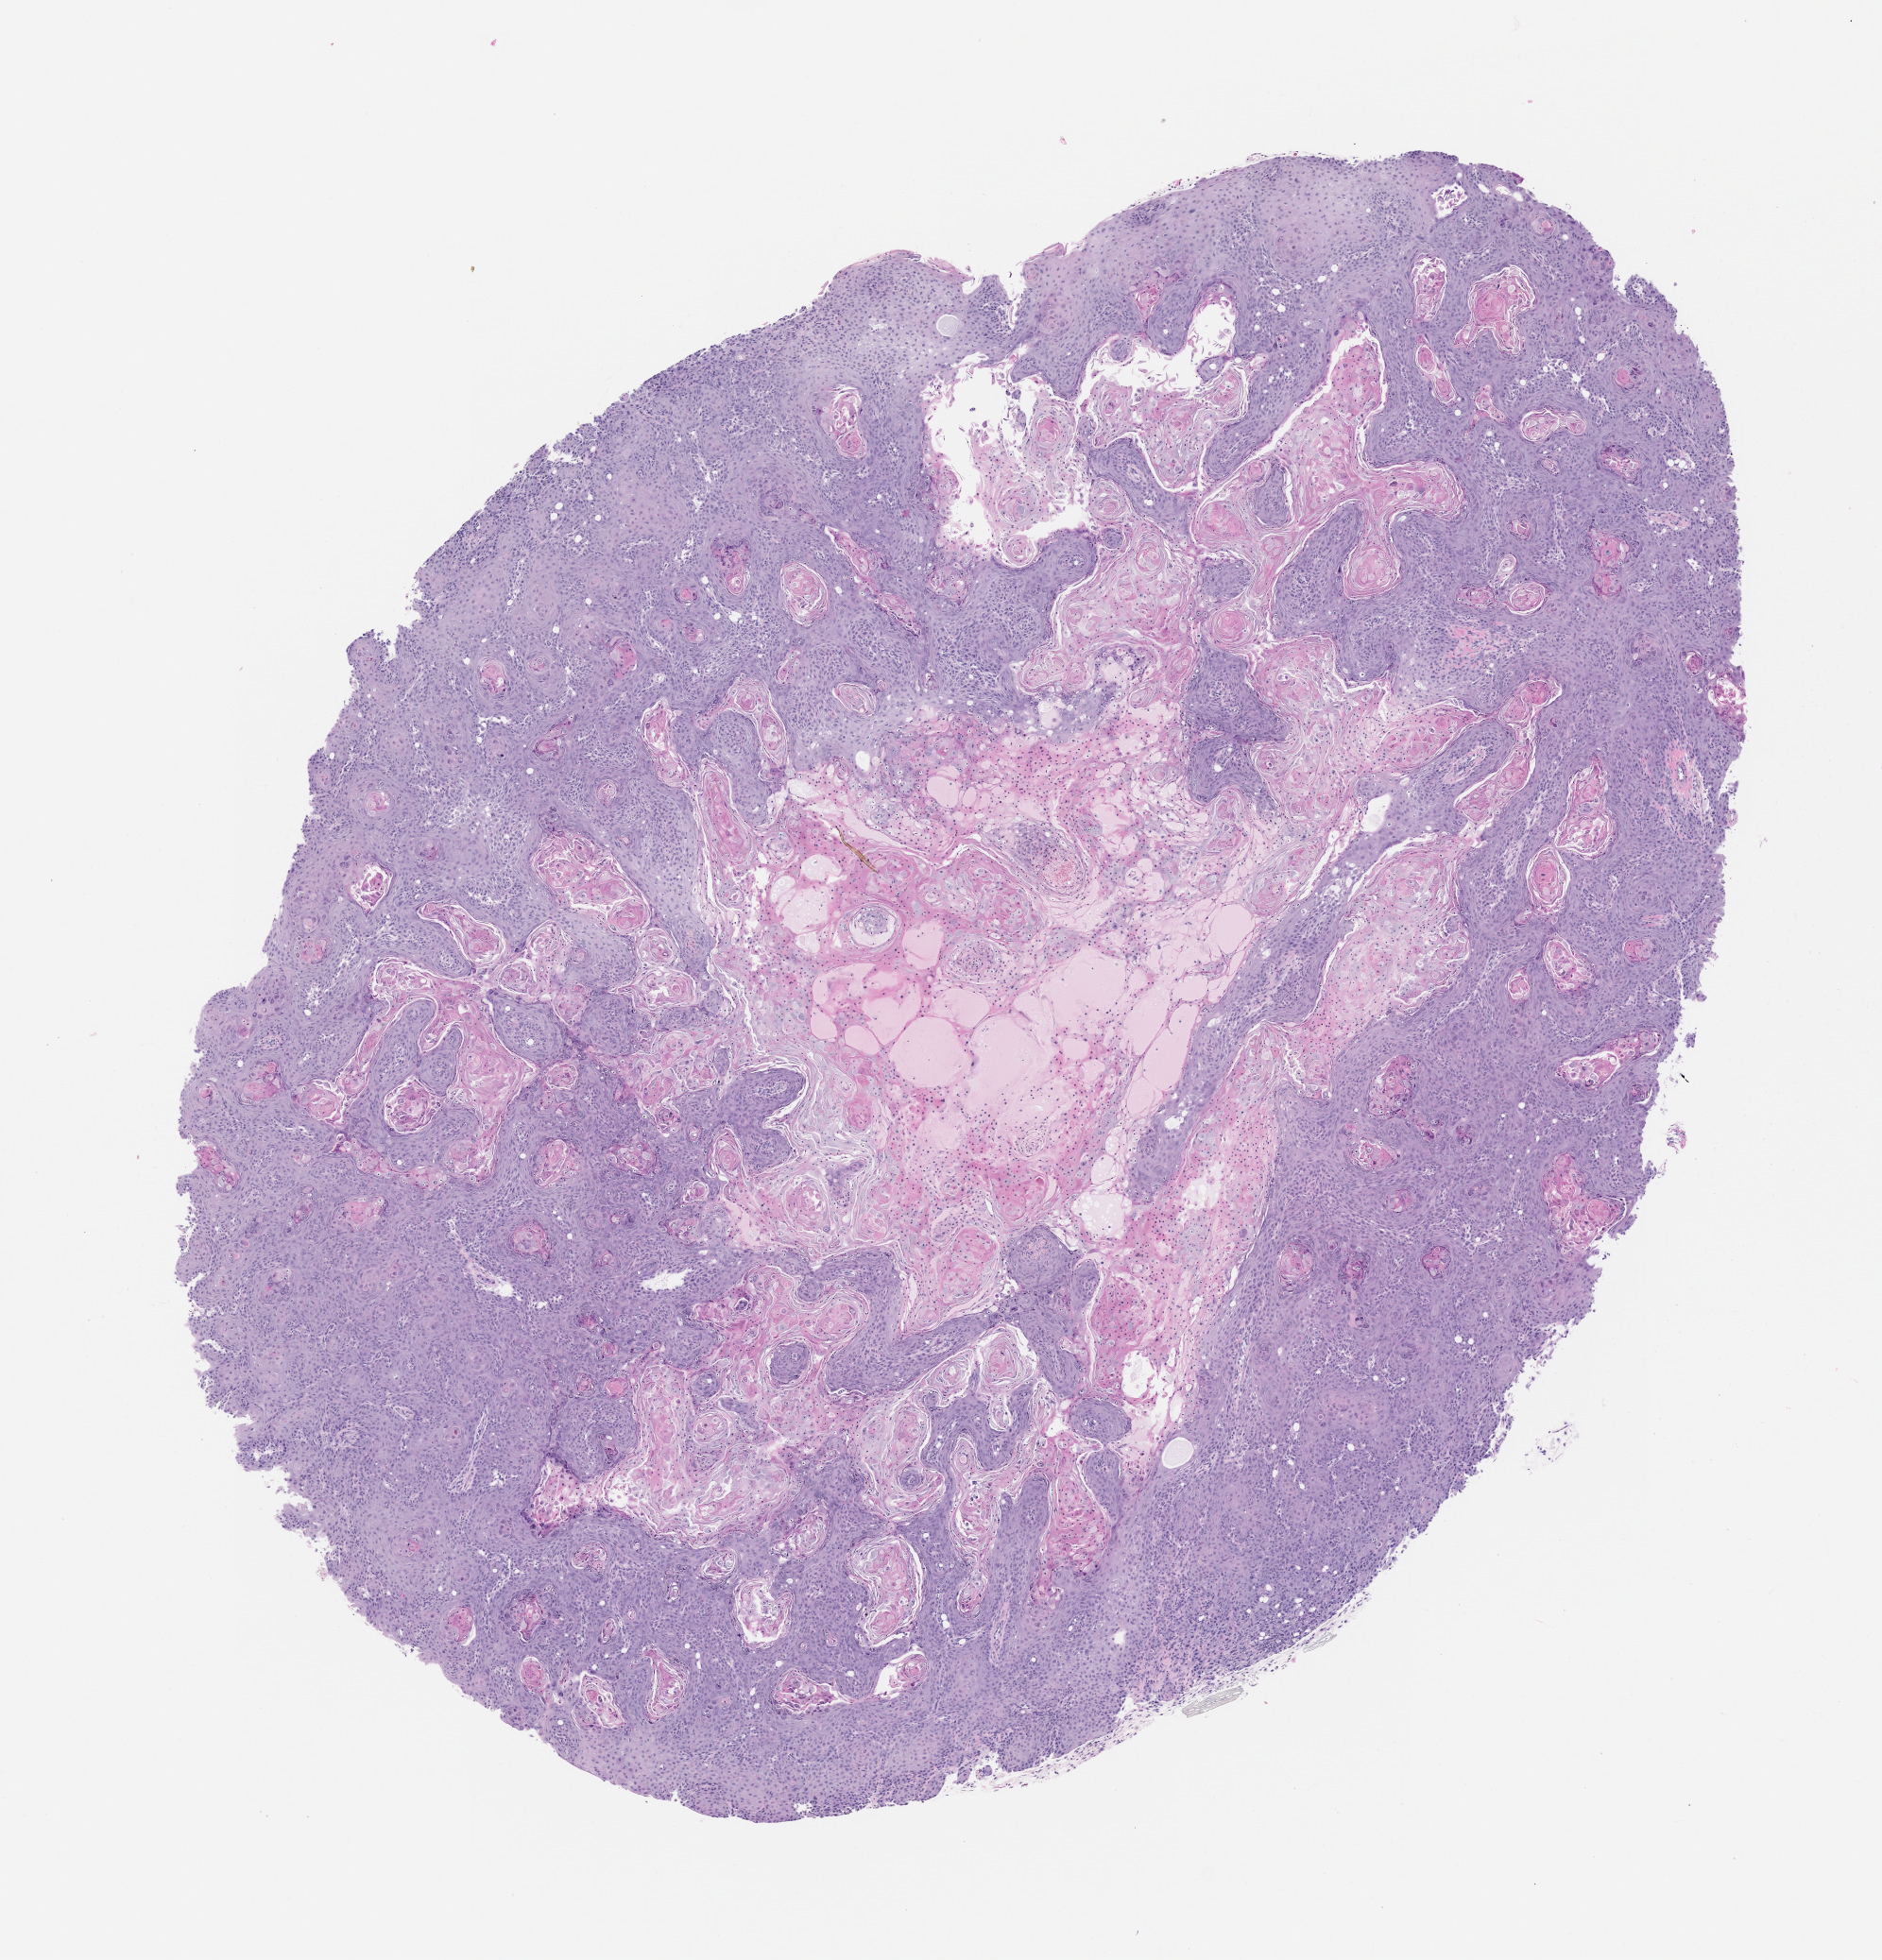
H&E whole-slide image of a patient-derived xenograft (PDX) tumor grown in a mouse, passage 2 — a low-resolution overview of the entire scanned area, about 8.0 x 8.3 mm; formalin-fixed, paraffin-embedded (FFPE) tissue; tumor site category: oral soft tissue.
* originating patient diagnosis: Head and Neck Squamous Cell Carcinoma